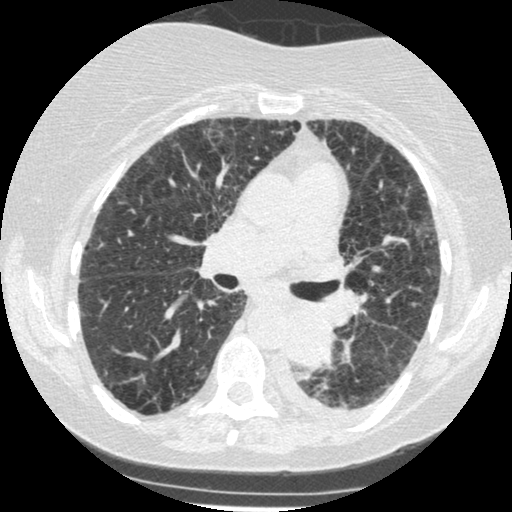
Low-dose screening chest CT, one axial slice; slice 147 of 341 in the series (ordered by position); lung window (W 1500 / L -600 HU); 1.25 mm slice thickness; 512 × 512 image matrix, field of view 310 × 310 mm.
Outlined on this slice (expert manual segmentation):
- lesion 1 (tumor, lower lobe of left lung): bounding box (x1, y1, x2, y2) in pixels: (286, 309, 335, 367)